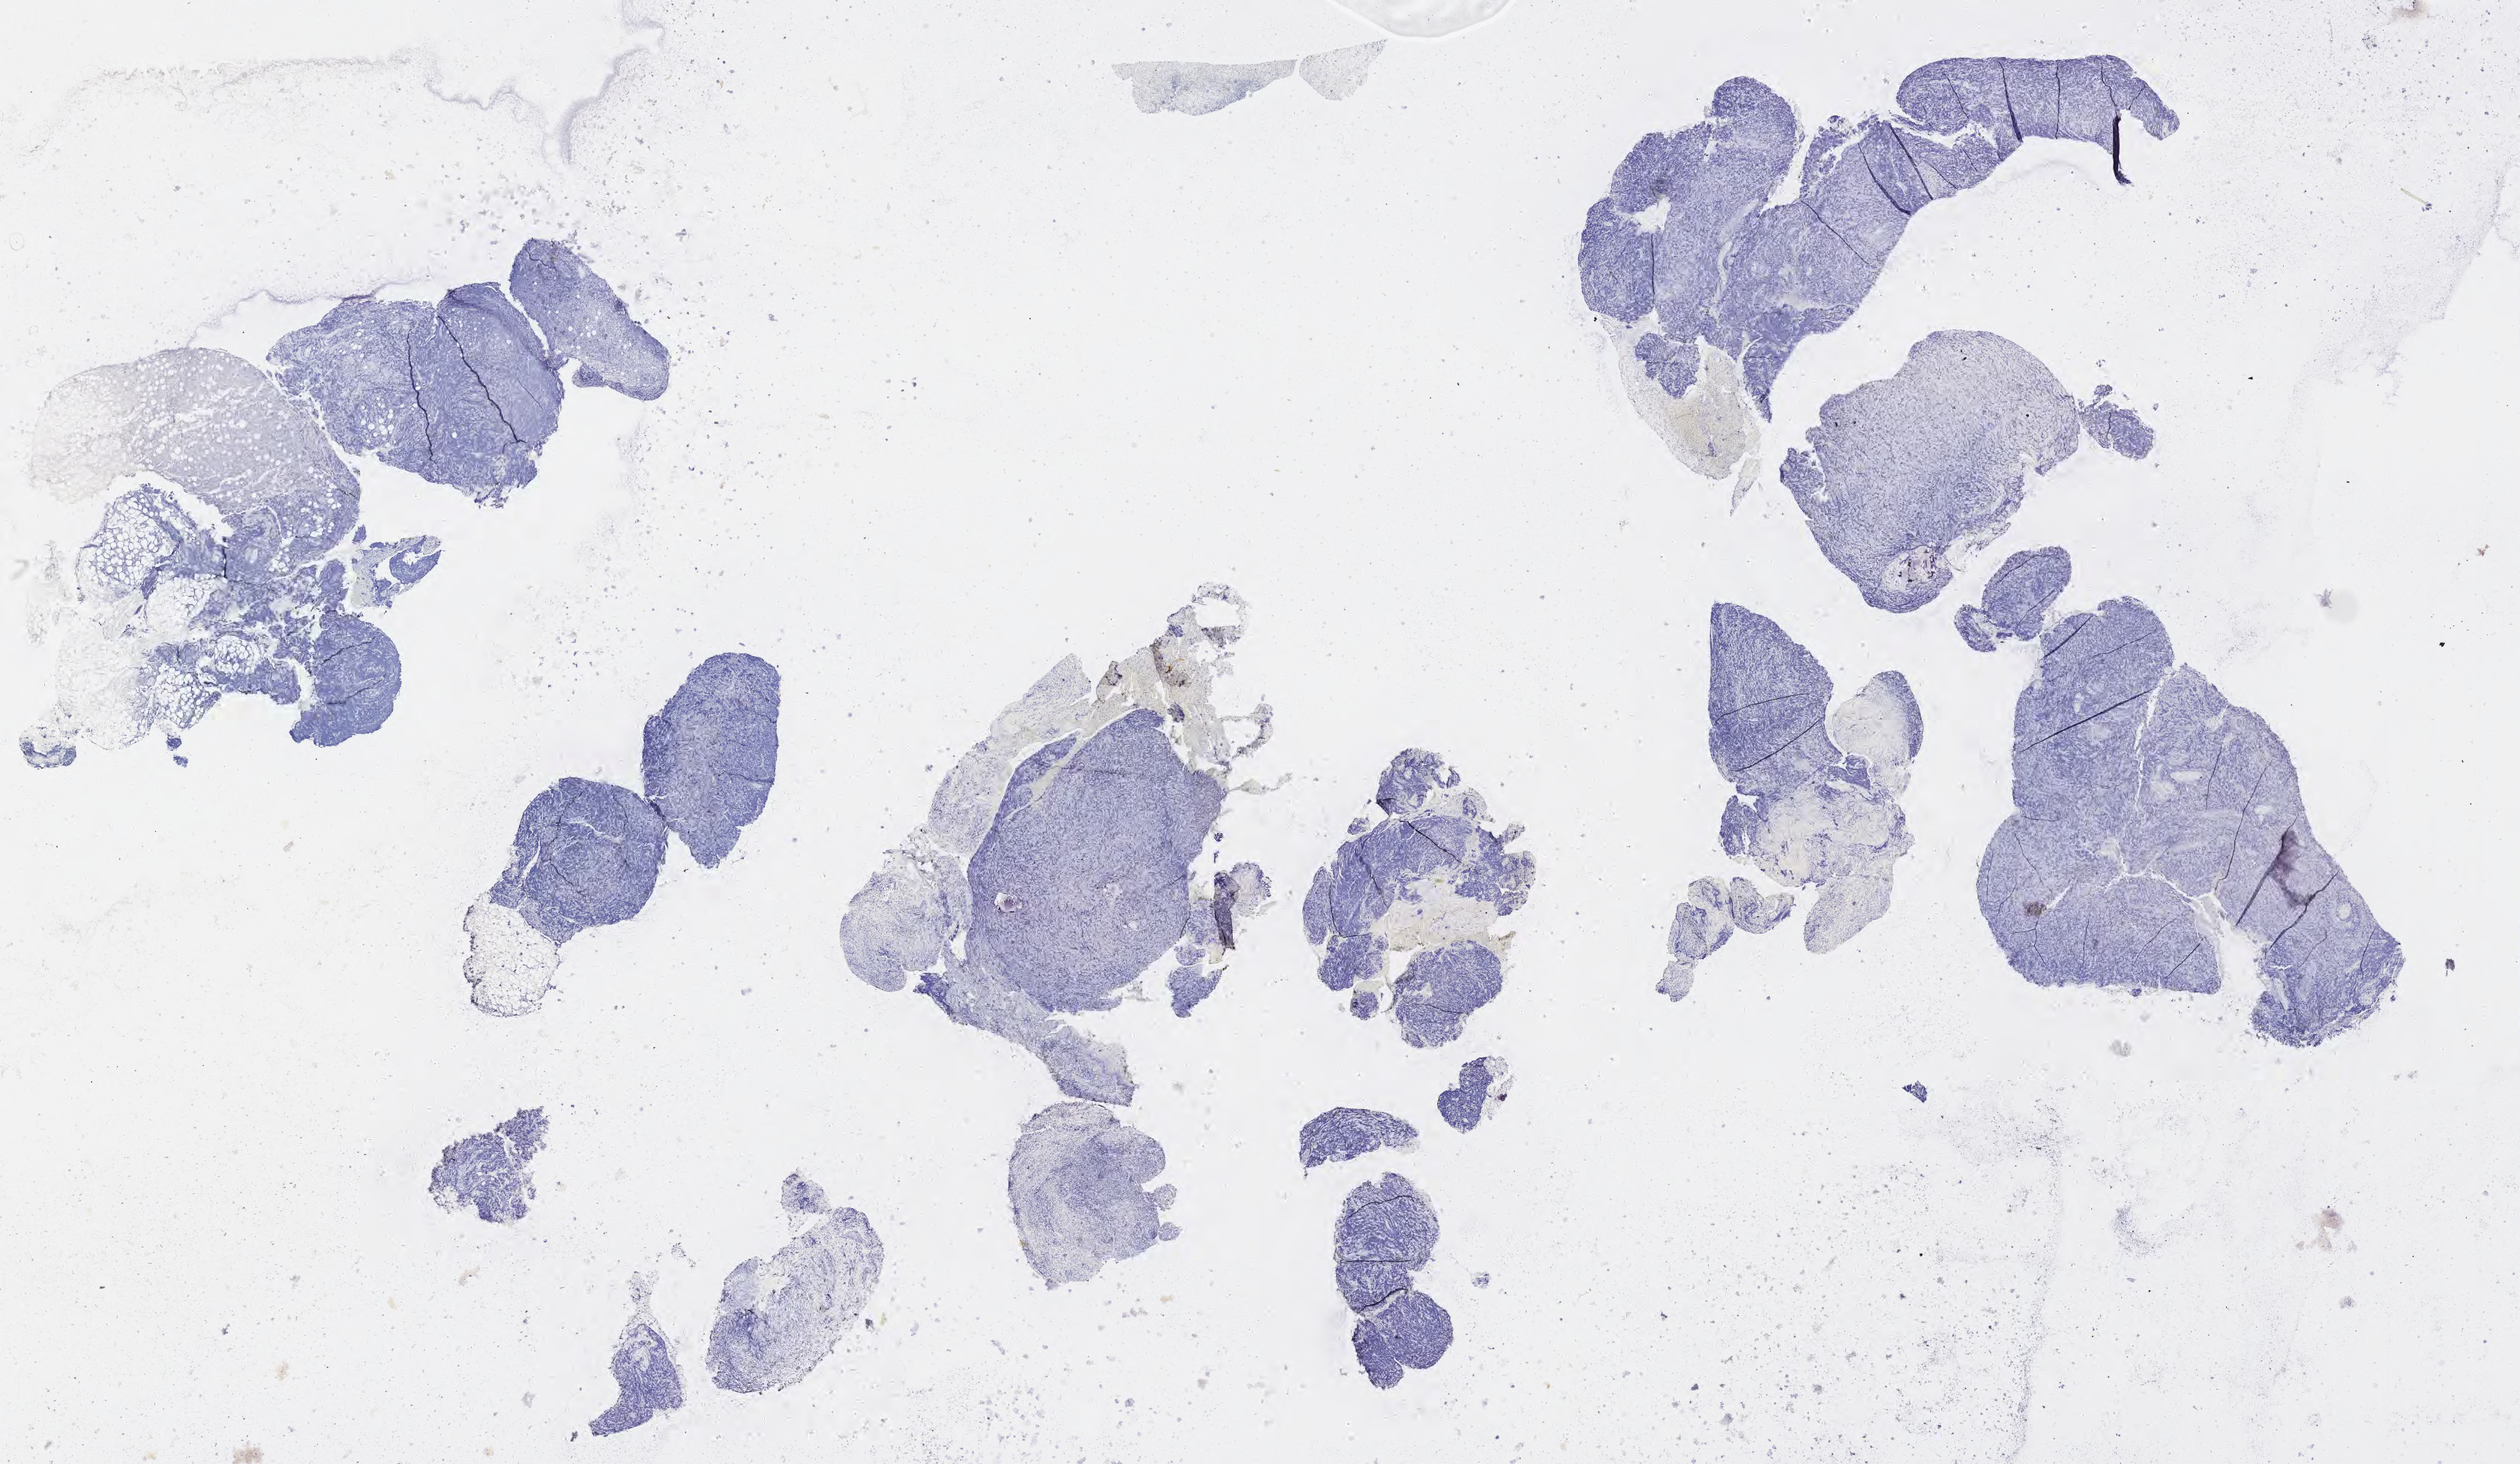
In-situ hybridisation whole-slide image, Epstein–Barr virus-encoded RNA (EBER) probe — low-resolution overview of the scanned area, about 27.2 x 15.8 mm. Specimen: tumor tissue. Patient male; age 45 years.
Histologic diagnosis: Diffuse large B-cell lymphoma, NOS.